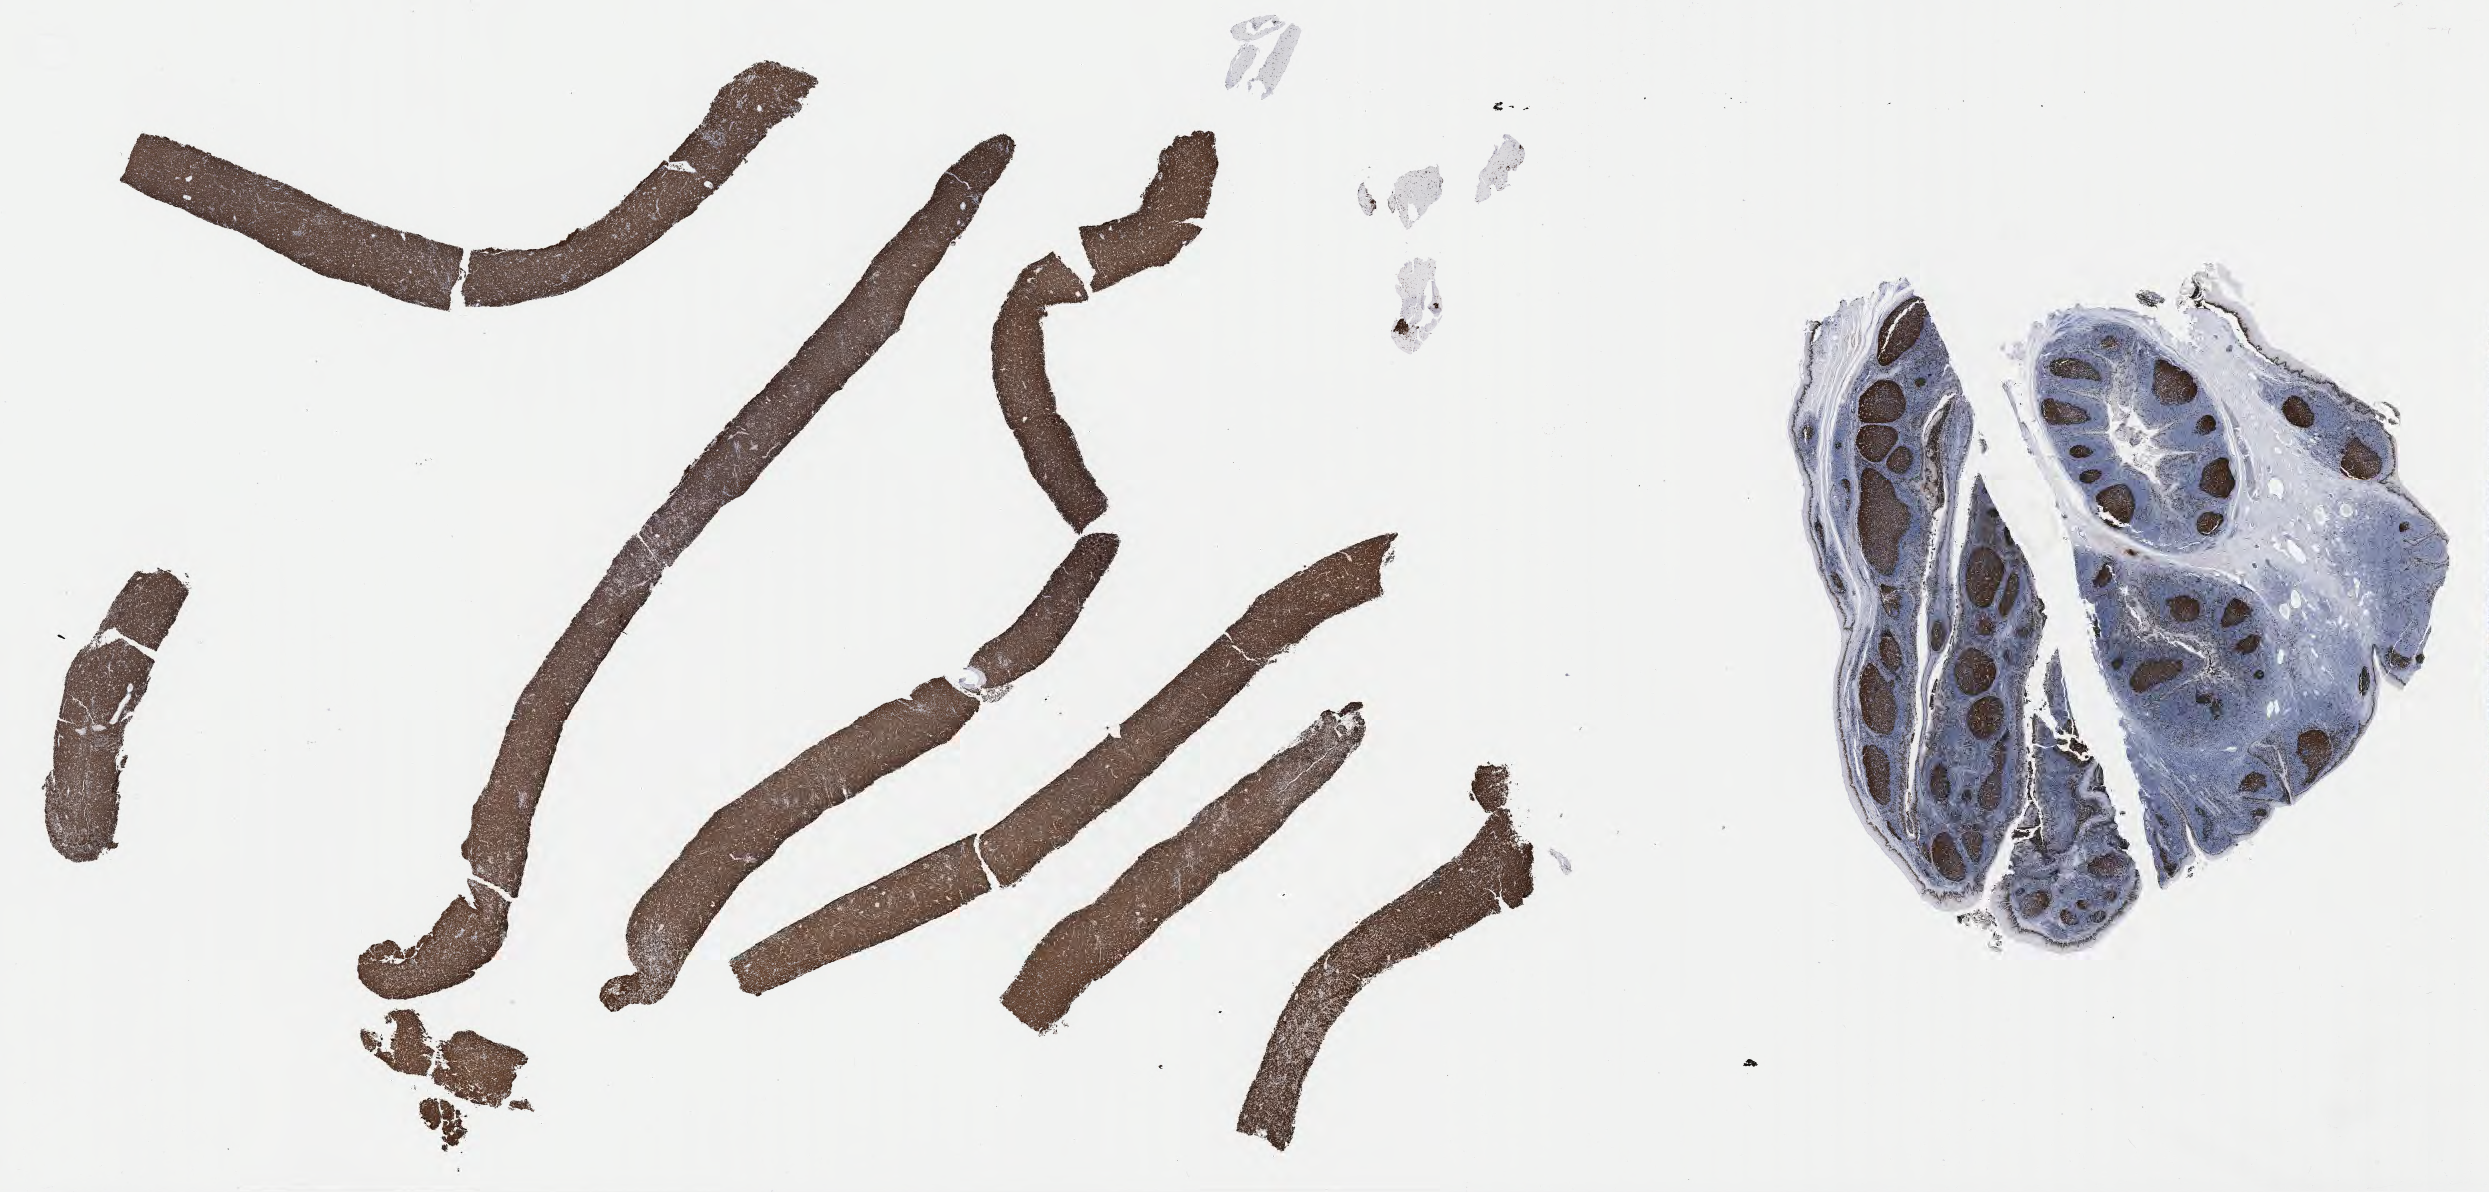
Whole-slide image, immunohistochemical stain for Ki-67 — a low-resolution overview of the entire scanned area, about 40.3 x 19.3 mm; specimen: tumor tissue. Patient: male, 29 years old.
* diagnosis: Burkitt lymphoma, NOS